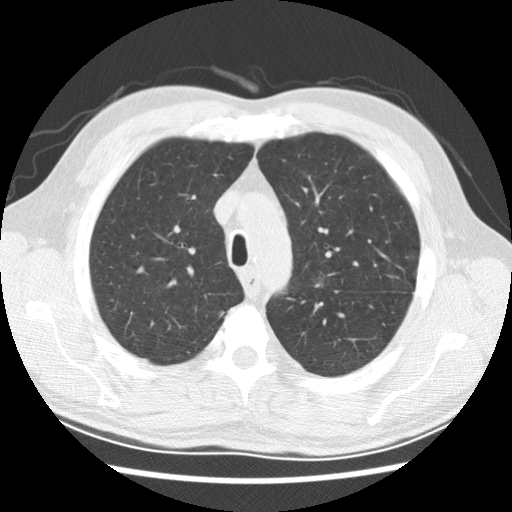
Axial slice from a low-dose chest CT screening exam; first (baseline) screen; lung window (W 1500 / L -600 HU); 2.5 mm slice thickness; 512 × 512 image matrix, field of view 340 × 340 mm. Male, age 59 years at enrolment.
Expert reader's lesion annotation, bounding box [x1, y1, x2, y2] px = [303, 266, 341, 297]. Reader record for this screening exam (exam-level; its link to the box is not recorded): non-calcified nodule or mass ≥4 mm, left upper lobe, 8 × 5 mm, smooth margins, soft tissue attenuation. Official screen result: positive, change unspecified: nodule(s) >= 4 mm or enlarging nodule(s), mass(es), or other non-specific abnormalities suspicious for lung cancer. Participant outcome: lung cancer diagnosed 645 days after this screen — adenocarcinoma, NOS, left upper lobe, left lower lobe, poorly differentiated (G3), stage IV (AJCC 6th edition).